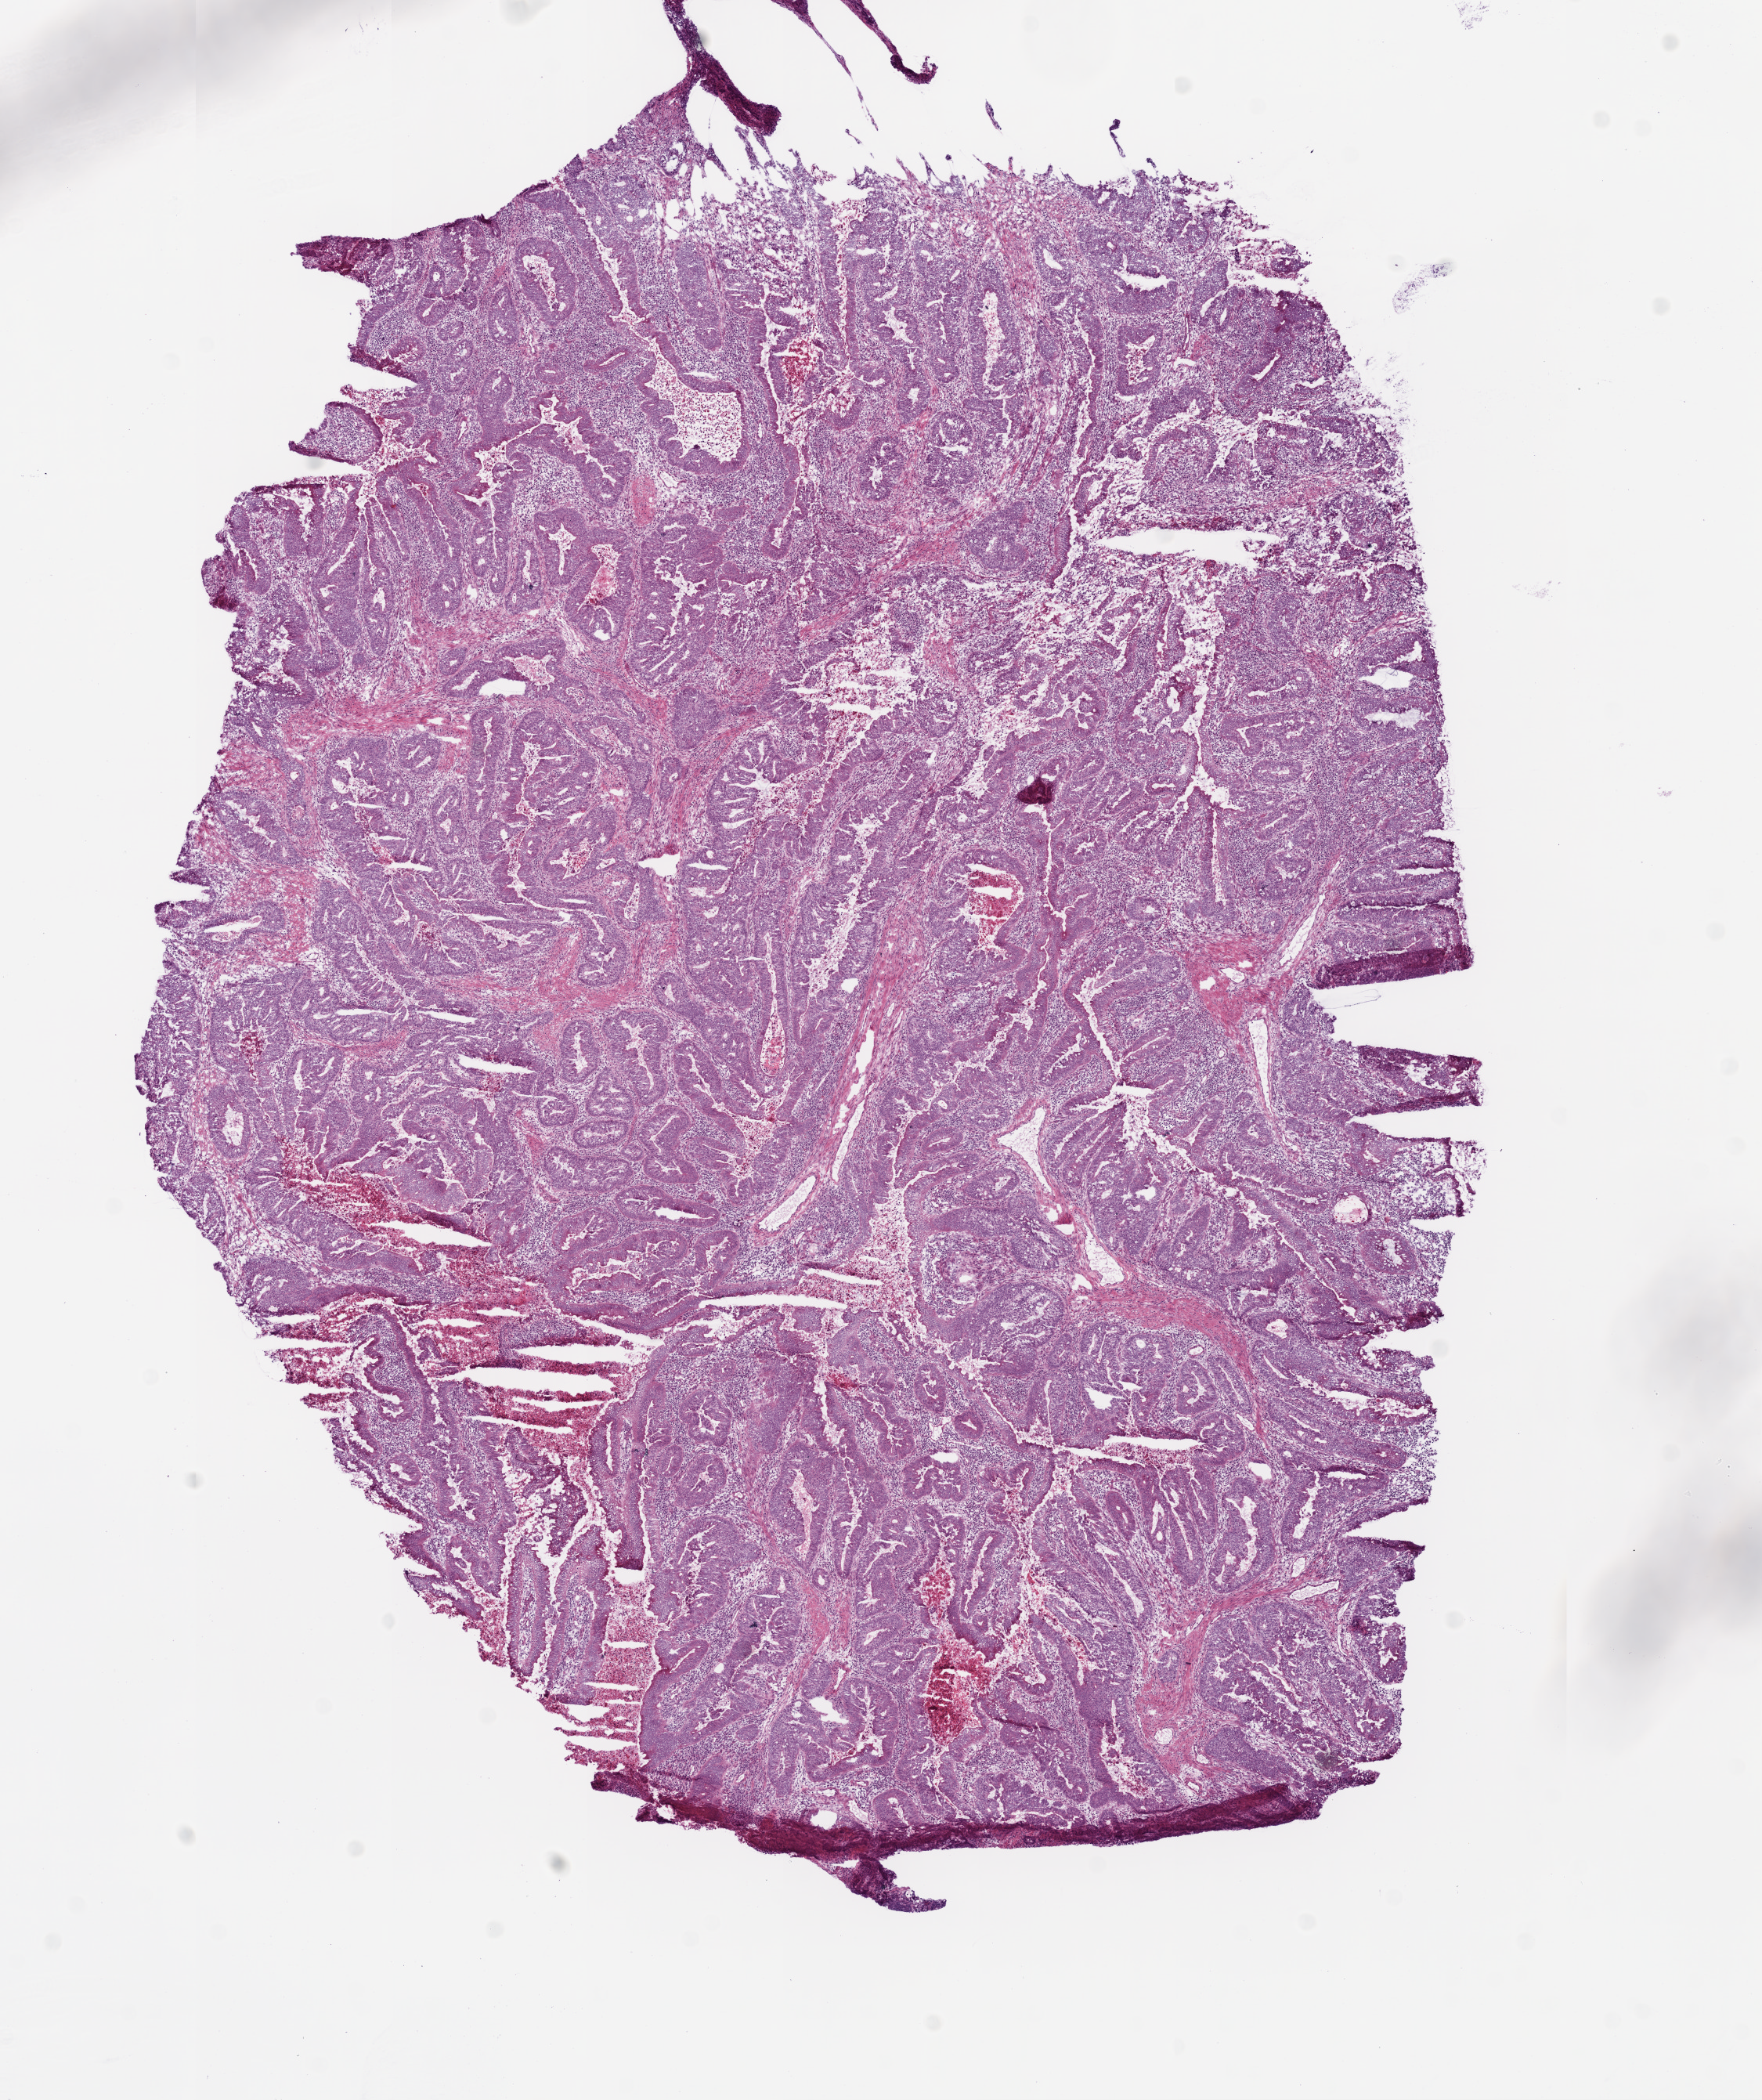
Whole-slide histology image, H&E-stained, whole scanned area (about 9.0 x 10.8 mm, slide scanned at 20x) shown as a low-resolution overview, frozen section from the bottom of the tissue portion, sample: primary tumour, colon. Male patient; age at initial diagnosis 66 years. Slide review estimates, as recorded: tumour cells 85%, tumour nuclei 70%, normal cells 0%, stromal cells 10%, necrosis 5%.
Pathologic diagnosis: Adenocarcinoma, NOS. AJCC pathologic stage: IIA. Lymph nodes positive (case pathology): 0 of 12 examined.